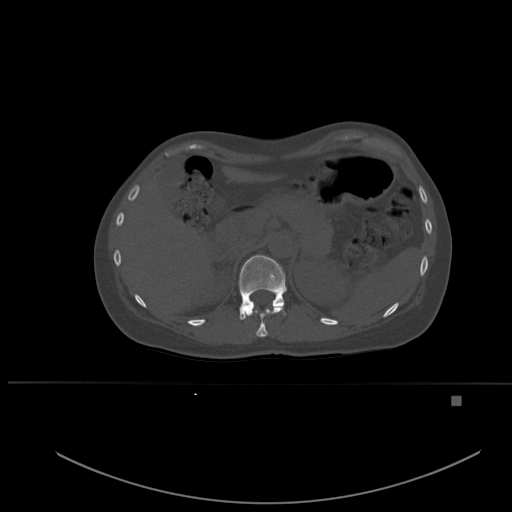
CT including the spine, one axial slice. Slice 261 of 651 in the series (ordered by position). Bone window (W 1800 / L 400 HU). 512 × 512 image matrix. Patient: female, 49 years. From the clinical record (not read from this slice): primary cancer: breast.
Outlined on this slice (semi-automatic segmentation, software-assisted and operator-edited):
- T11 vertebra: bounding box [x1, y1, x2, y2] px = [246, 307, 284, 337]
- T12 vertebra: [239, 255, 287, 320]